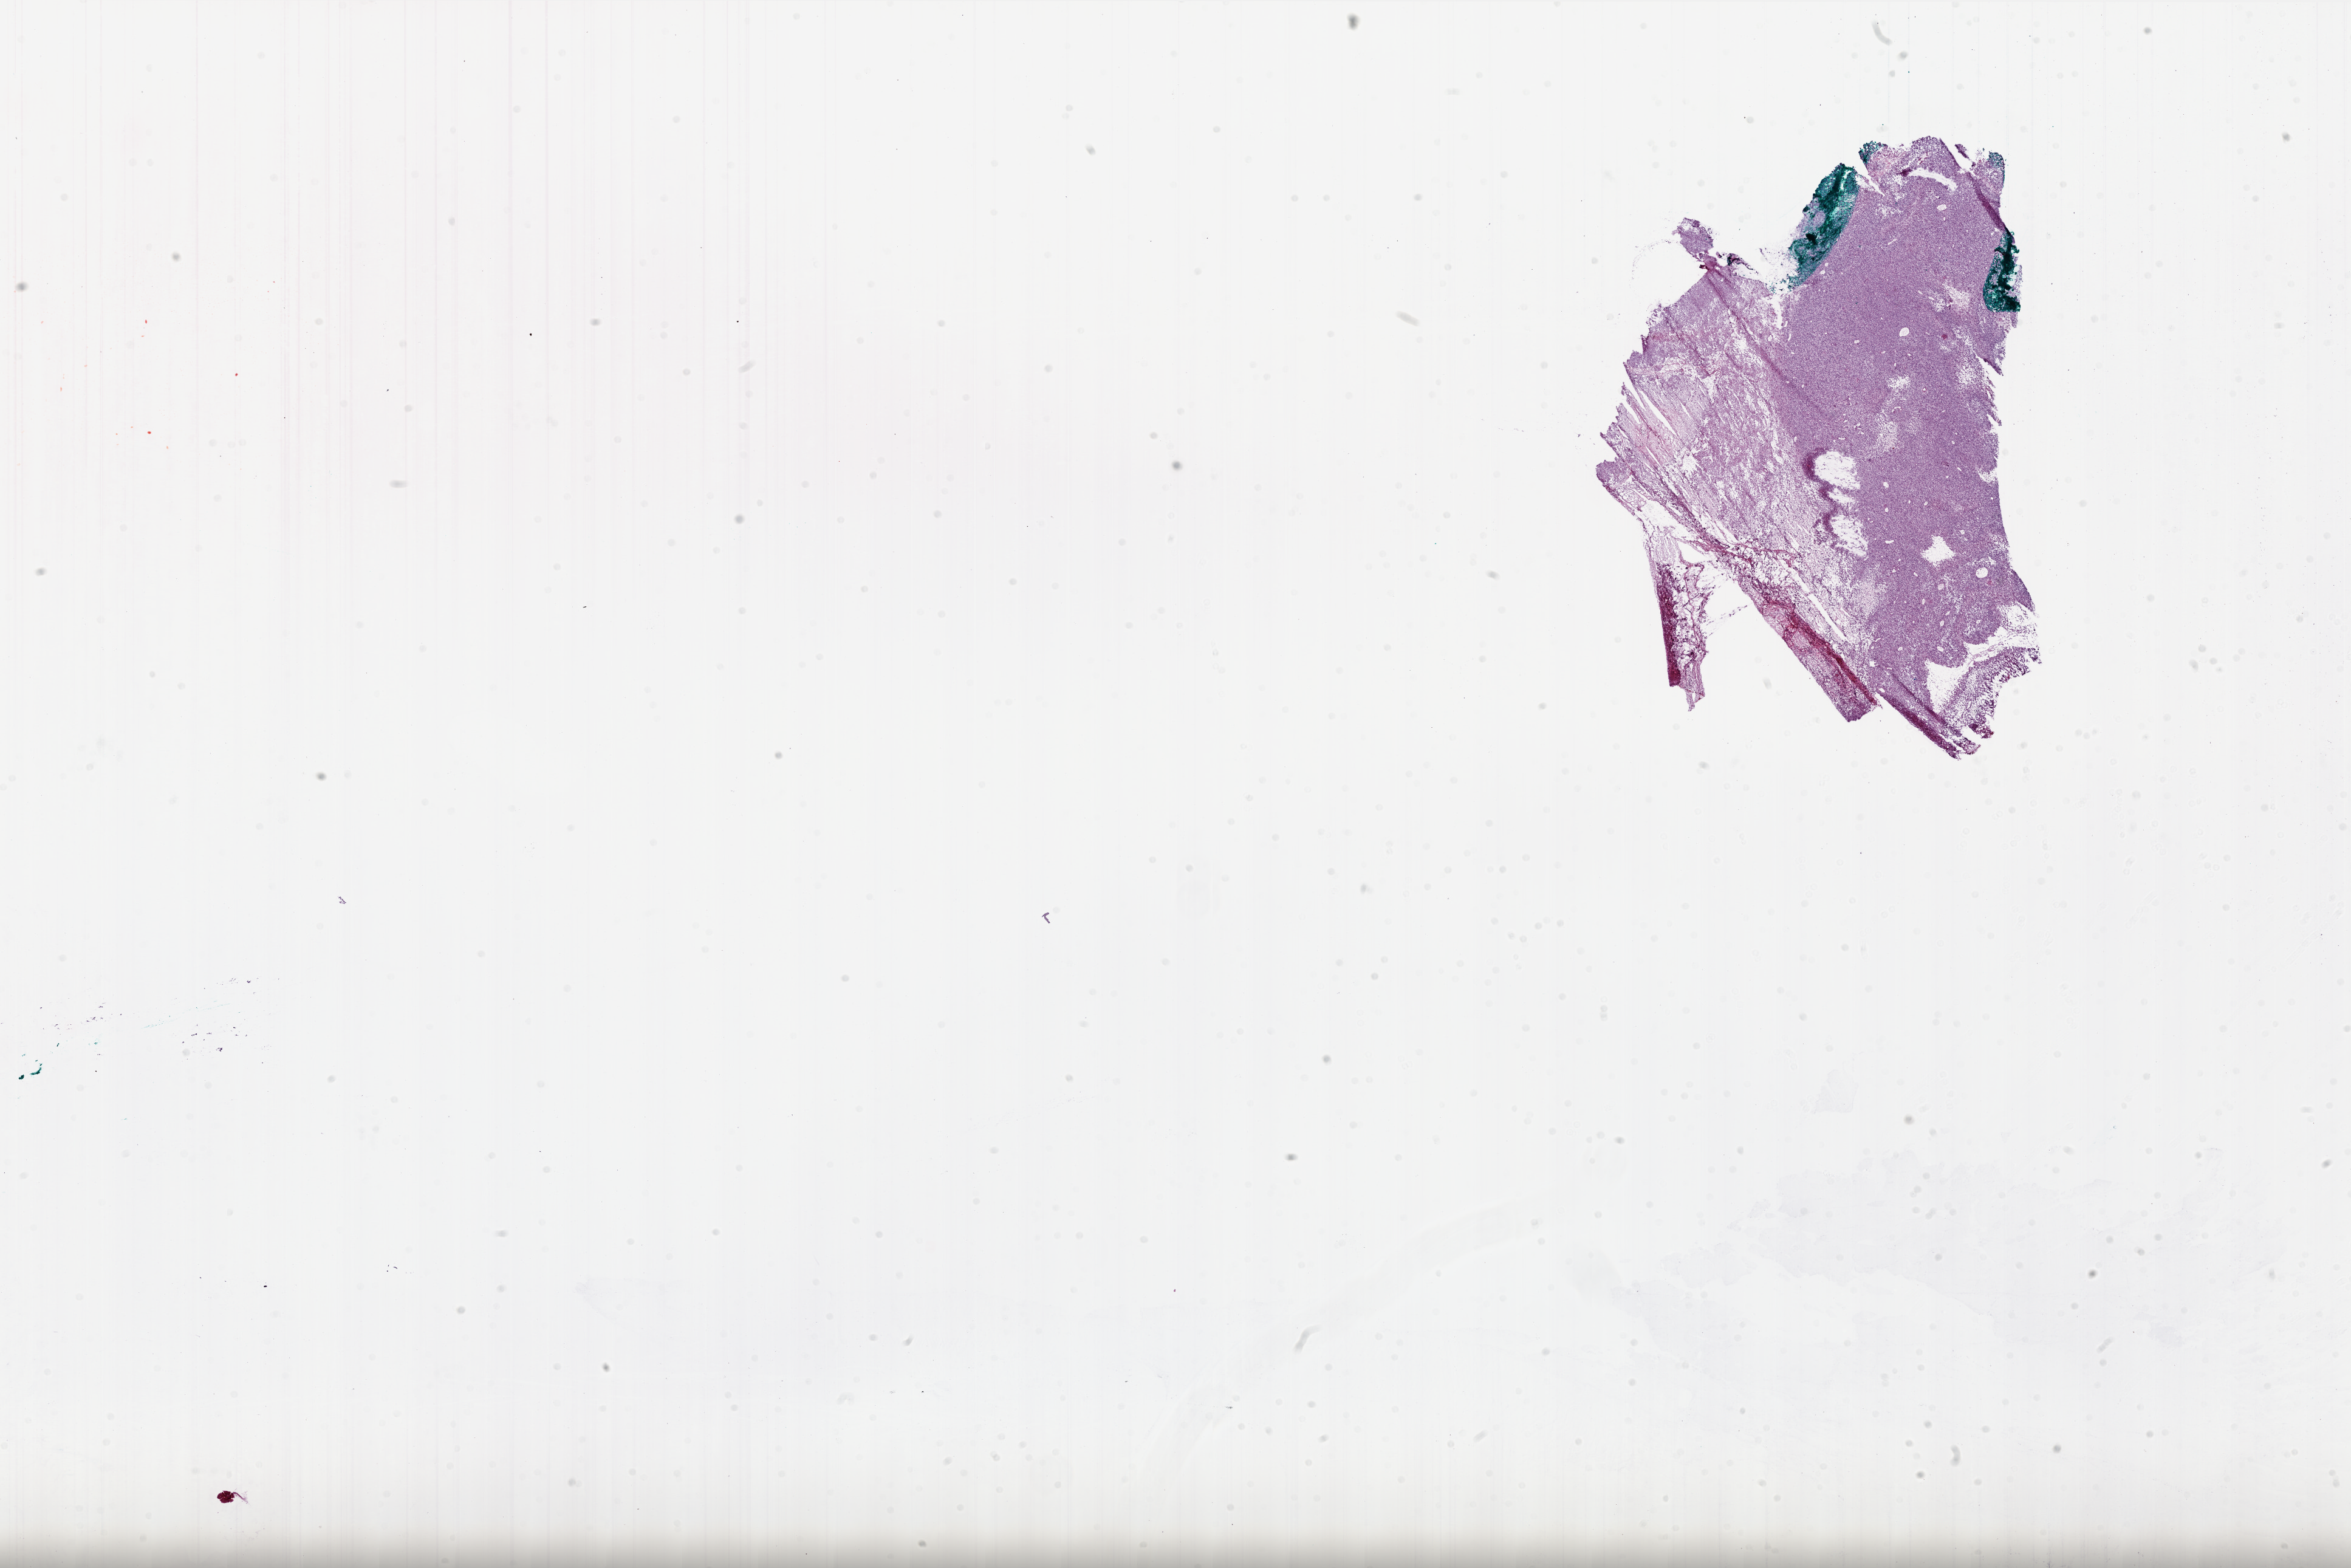
Digitized H&E-stained tissue section (whole slide) — whole scanned area (about 31.0 x 20.7 mm, acquisition: 20x scan) shown as a low-resolution overview; frozen section from the bottom of the tissue portion; sample: primary tumour, brain. Female, age 57 years at initial diagnosis. Pathologist review of this section (percent, as recorded): tumour cells 75%, tumour nuclei 90%, normal cells 0%, stromal cells 5%, necrosis 20%.
Pathologic diagnosis: Glioblastoma.